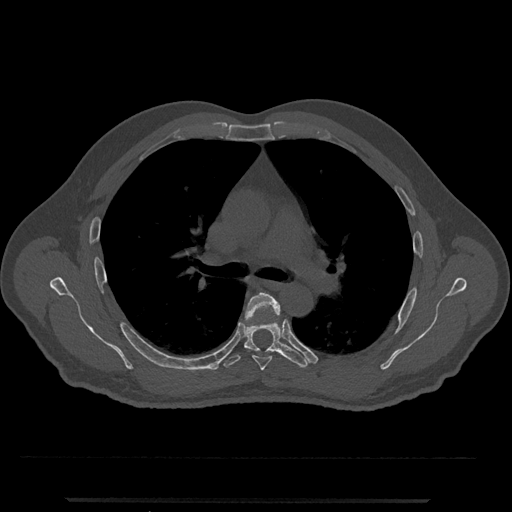
CT including the spine, one axial slice. Position 764 of 797 along the scan axis. Reconstruction kernel Br40s/3. 120 kVp. Bone window (W 1800 / L 400 HU). 0.5 mm slice thickness. 512 × 512 image matrix, field of view 419 × 419 mm. Patient: male, 63 years. Case-level facts recorded for this patient, not image findings: primary cancer: prostate.
Structures marked on this image (semi-automatically segmented with operator editing):
- T5 vertebra: box from (x=245, y=292) to (x=280, y=371) px
- T6 vertebra: (x=223, y=317)–(x=309, y=368)